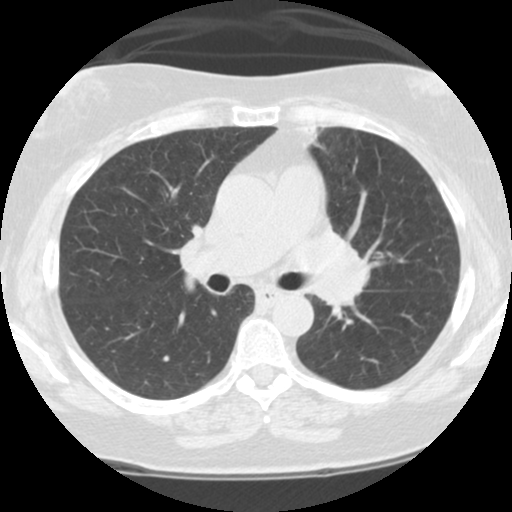
Low-dose screening chest CT, one axial slice; slice 65 of 108 in the series (ordered by position); reconstruction kernel STANDARD; 120 kVp; lung window (W 1500 / L -600 HU); 2.5 mm slice thickness; 512 × 512 image matrix, field of view 300 × 300 mm.
Outlined on this slice (manually delineated by an expert):
- lesion 1 (tumor, hilum of left lung): bounding box [x1, y1, x2, y2] px = [309, 232, 379, 322]